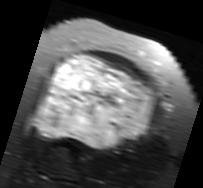
MRI of an extremity soft-tissue mass, one axial slice. Slice 49 of 91 in the series (ordered by position). T2-weighted fat-saturated. MR volume resampled by the dataset authors to the PET/CT grid (not the native acquisition matrix). 3.27 mm slice thickness. 203 × 188 image matrix, field of view 198 × 184 mm. Female patient. From the clinical record (not read from this slice): histological type: malignant solitary fibrous tumor; grade: intermediate; site of the primary tumour: right thigh.
Structures marked on this image (expert contour drawn on MRI and transferred to this co-registered scan by the dataset authors):
- gross tumour volume including surrounding oedema: box from (x=28, y=54) to (x=157, y=150) px
- gross tumour volume (mass): (x=33, y=54)–(x=155, y=148)